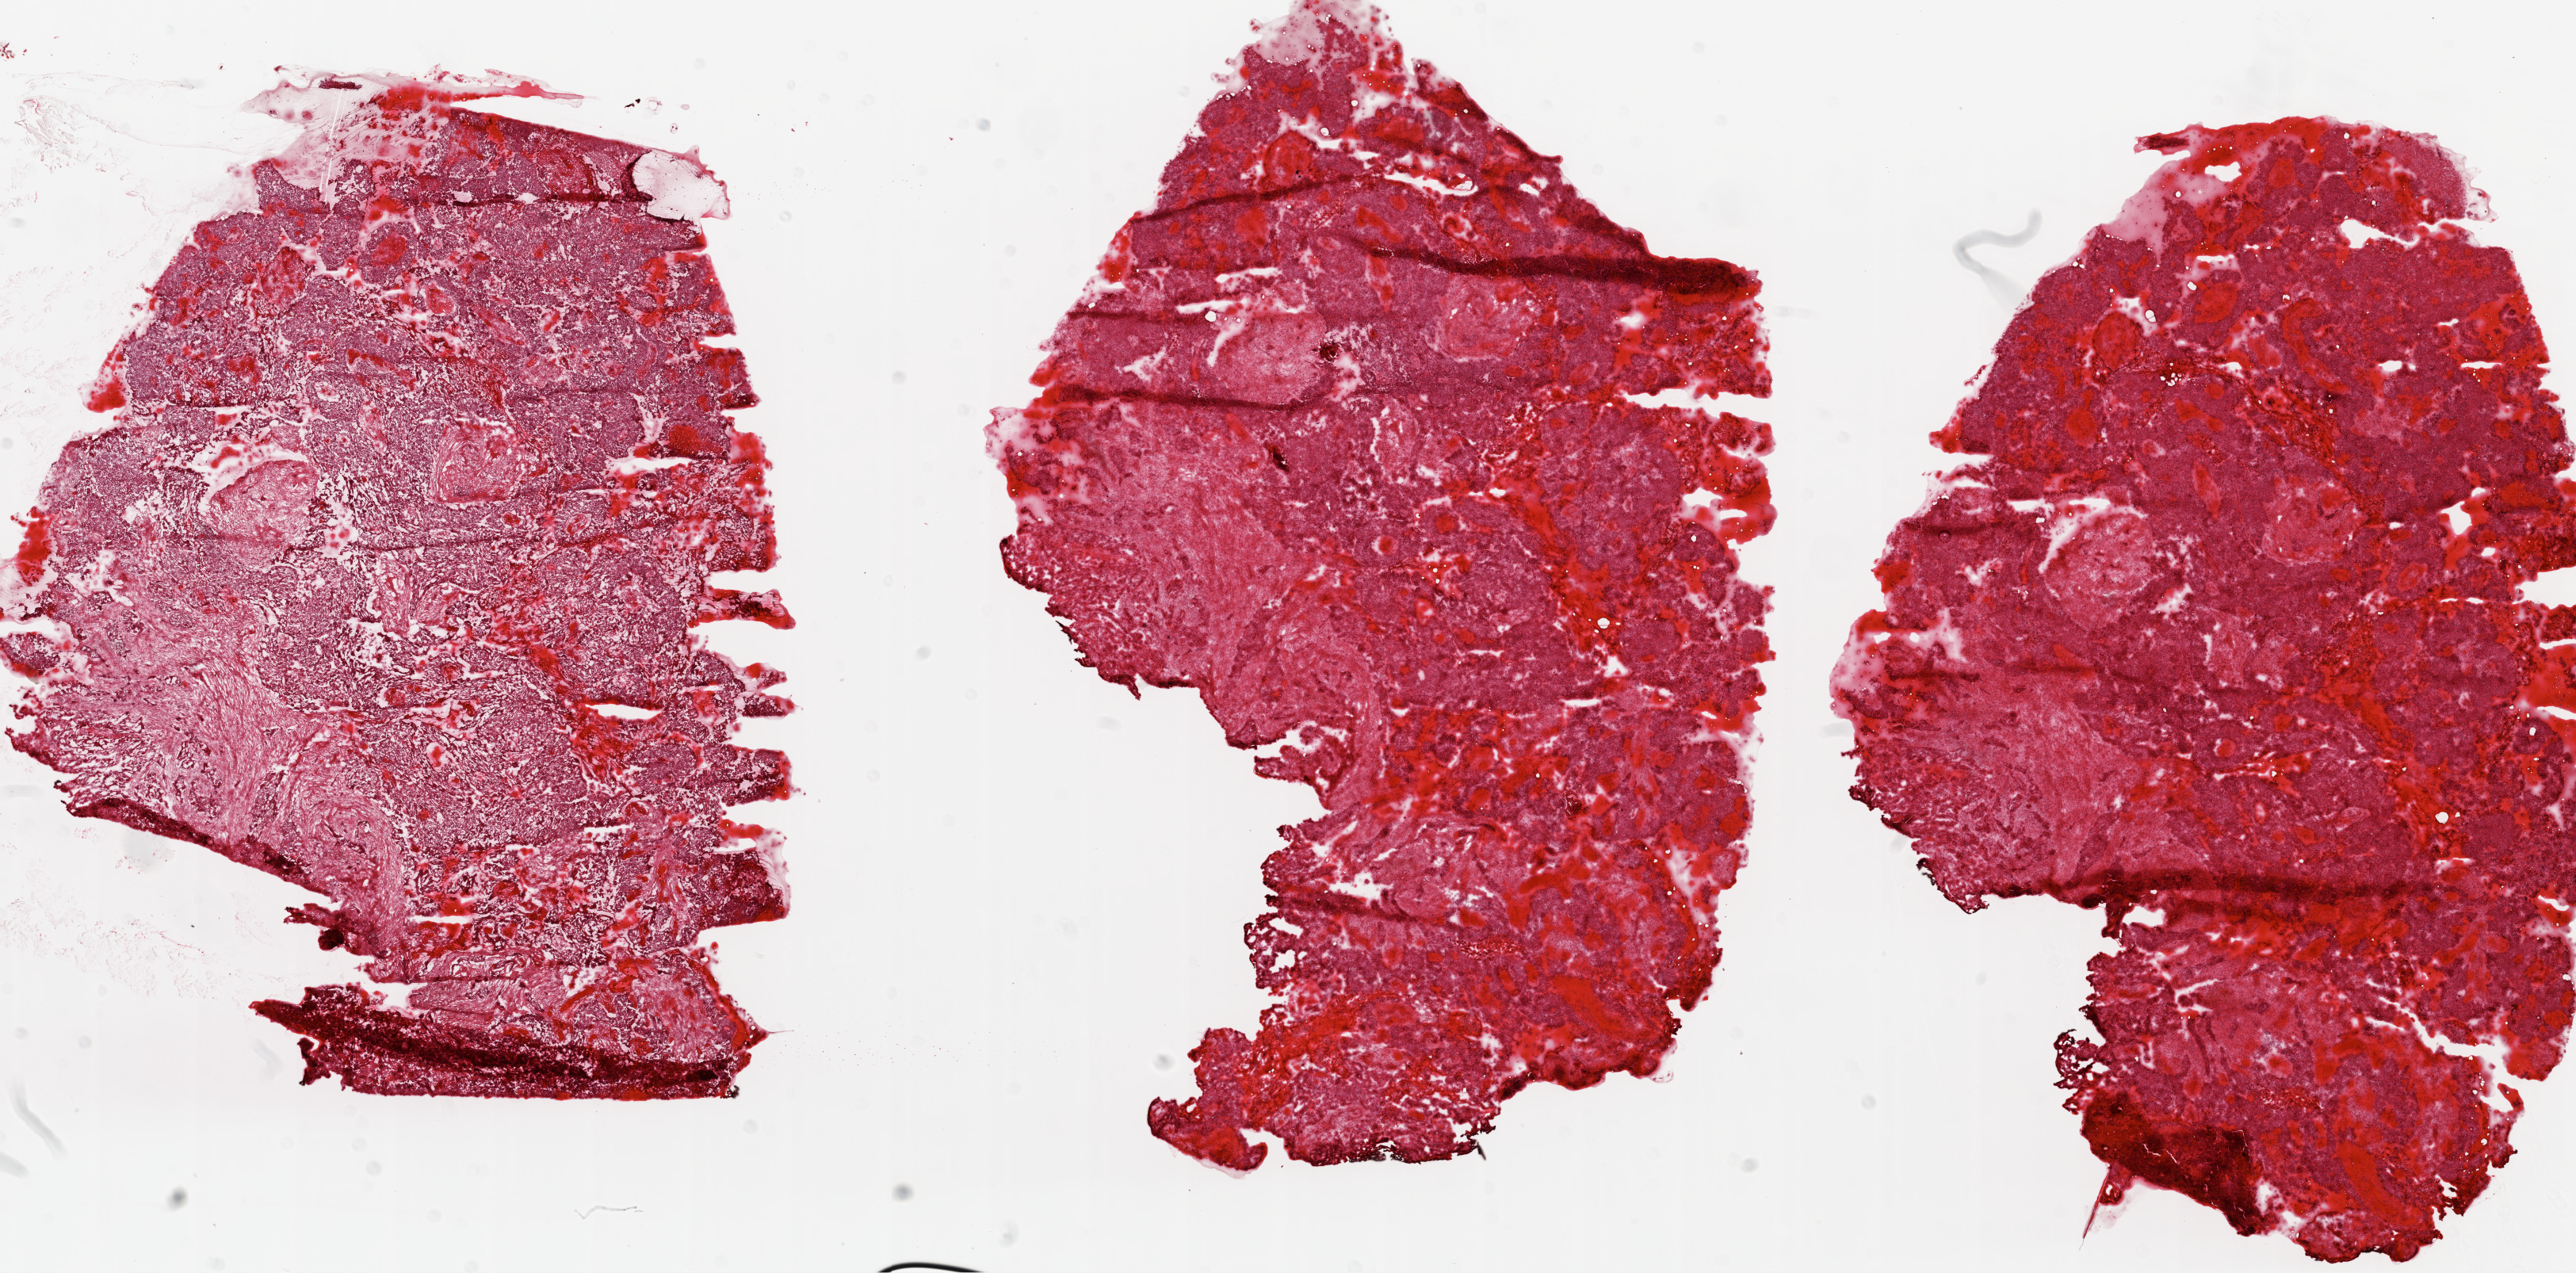
Hematoxylin and eosin (H&E) stained whole-slide image, a low-resolution overview of the entire scanned area, about 26.1 x 12.9 mm (acquisition: 20x scan), frozen section from the top of the tissue portion, sample: primary tumour, ovary. Female patient; age at initial diagnosis 66 years. Composition of this section per pathologist review: tumour cells 85%, tumour nuclei 90%.
Diagnosis: Serous cystadenocarcinoma, NOS.